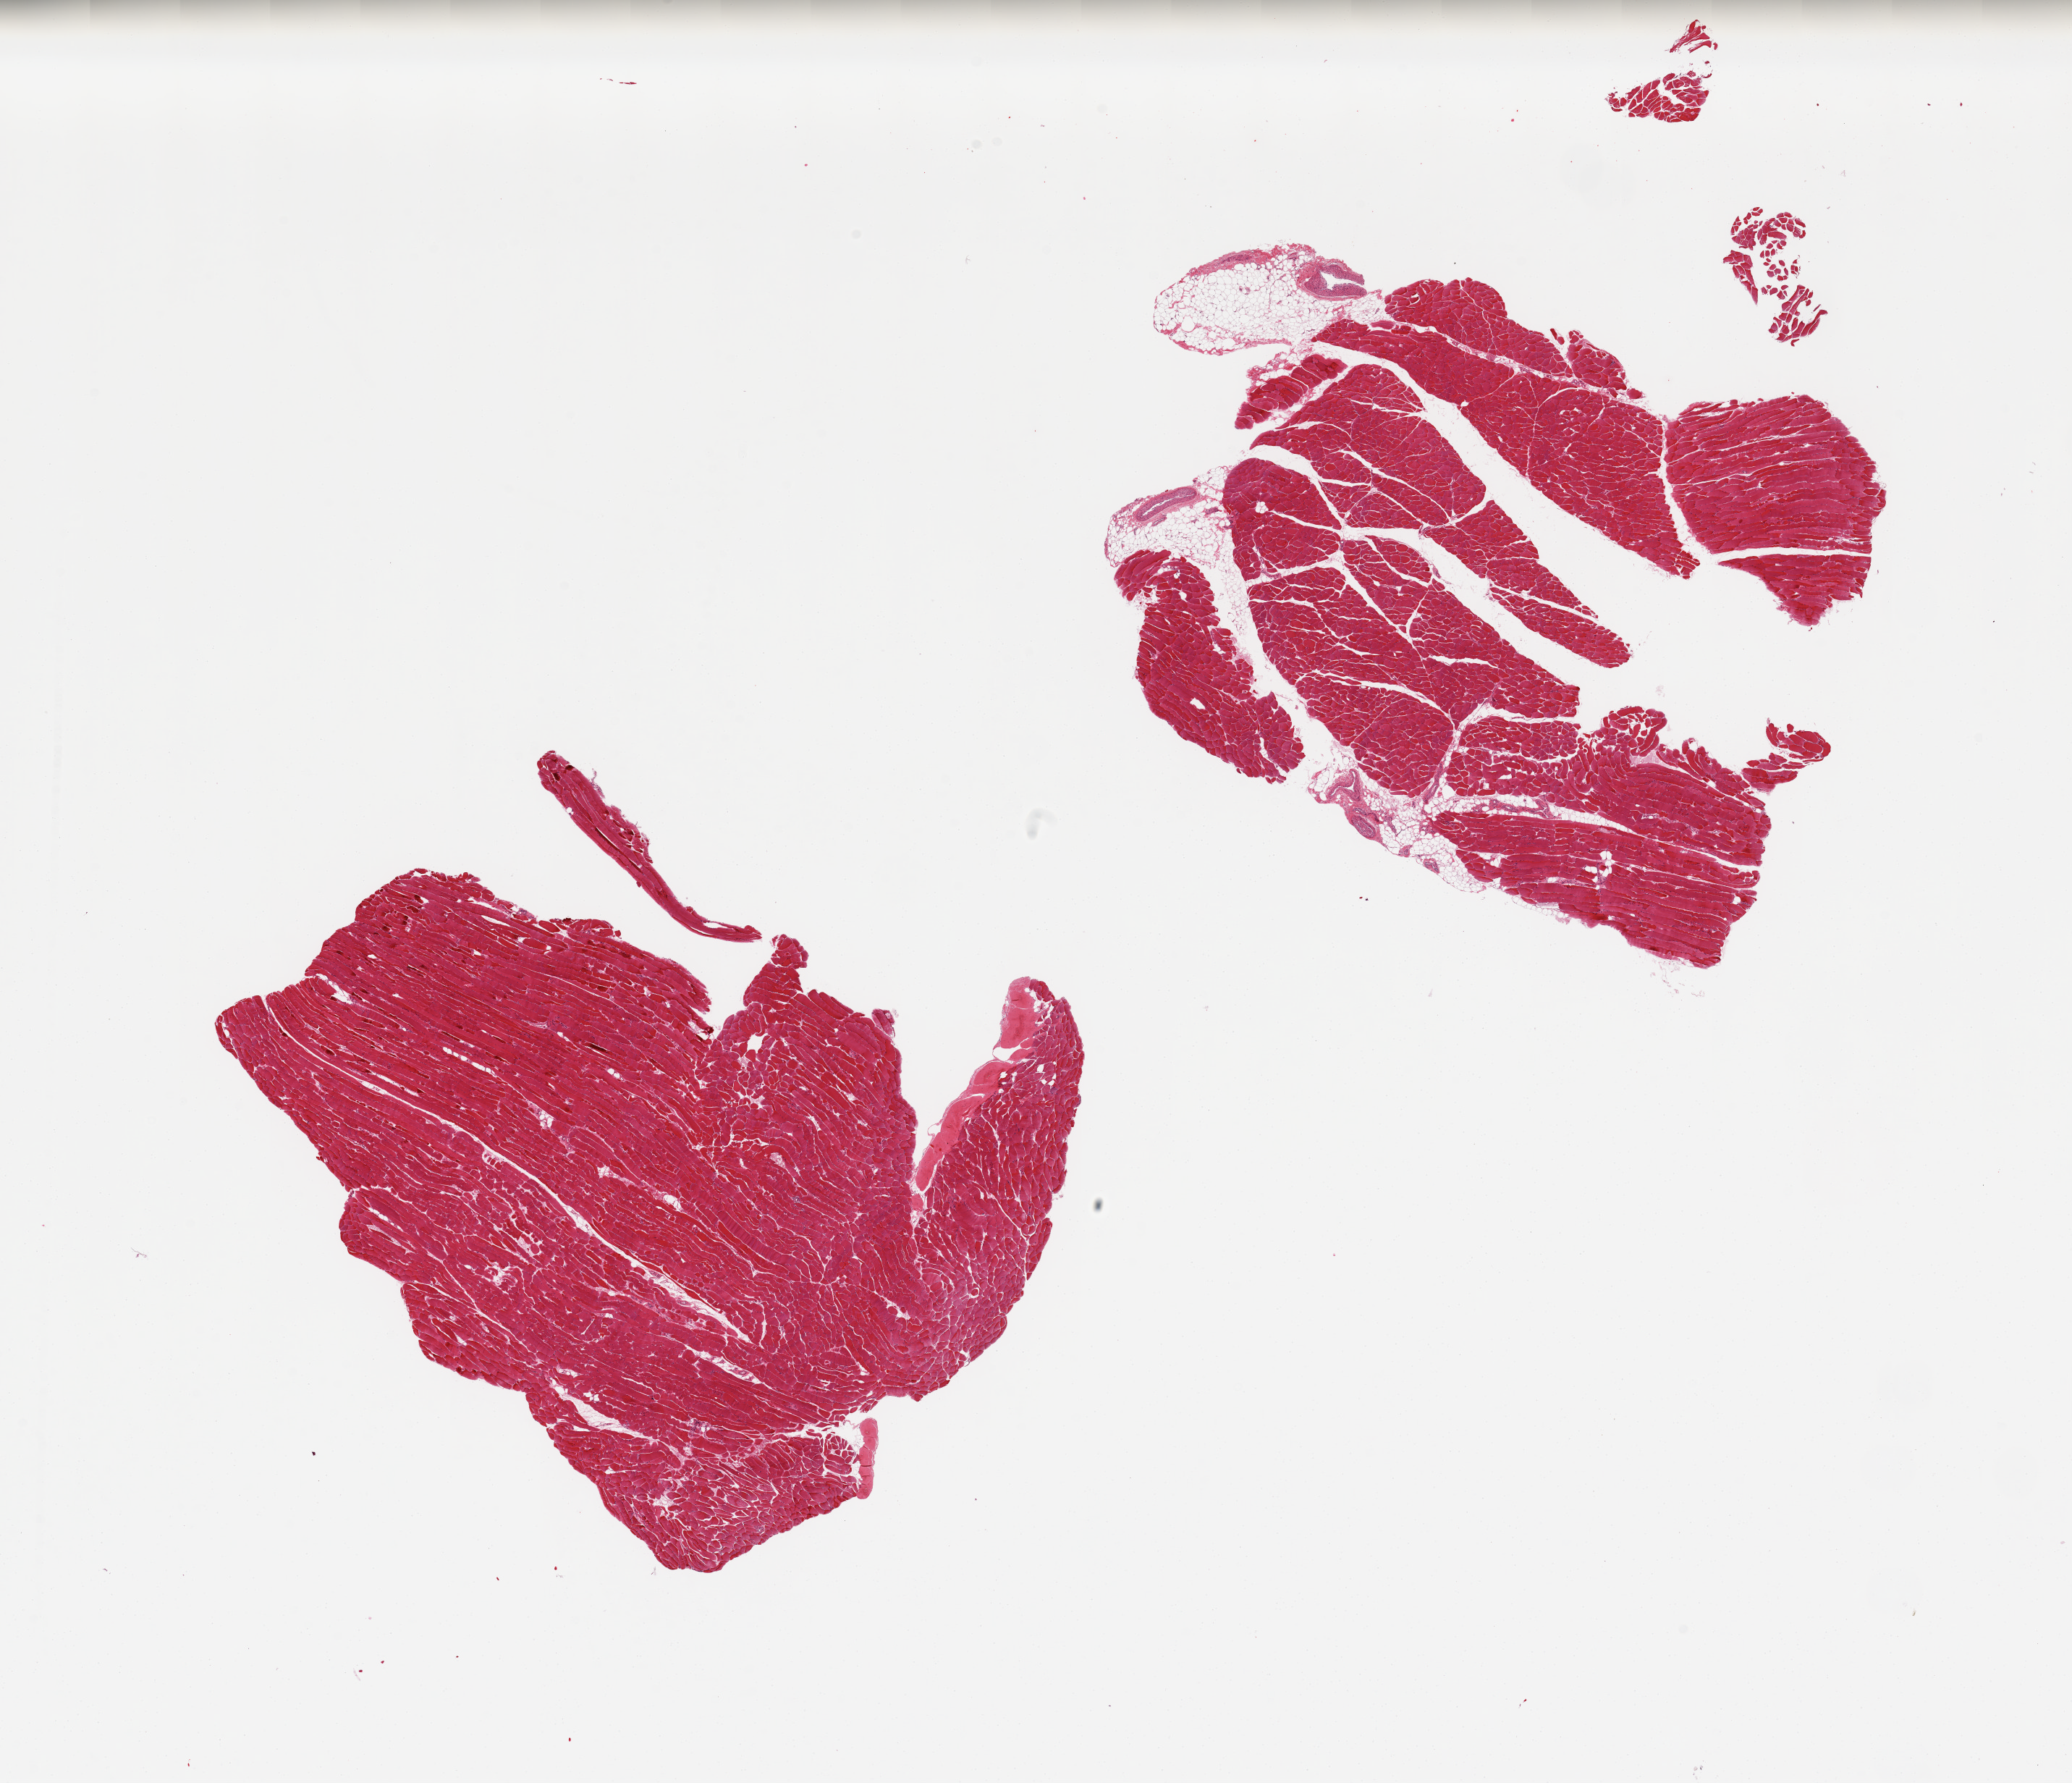
Digitized hematoxylin and eosin (H&E)-stained section, brightfield, a low-resolution overview of the entire scanned area, about 22.6 x 19.5 mm; PAXgene-fixed paraffin-embedded (PFPE) section; section of skeletal muscle (target tissue); donor tissue sample. Donor: female.
Pathologist's review note for this sample: 2 pieces, one includes ~20% internal and attached adipose tissue, one includes portion of tendon.